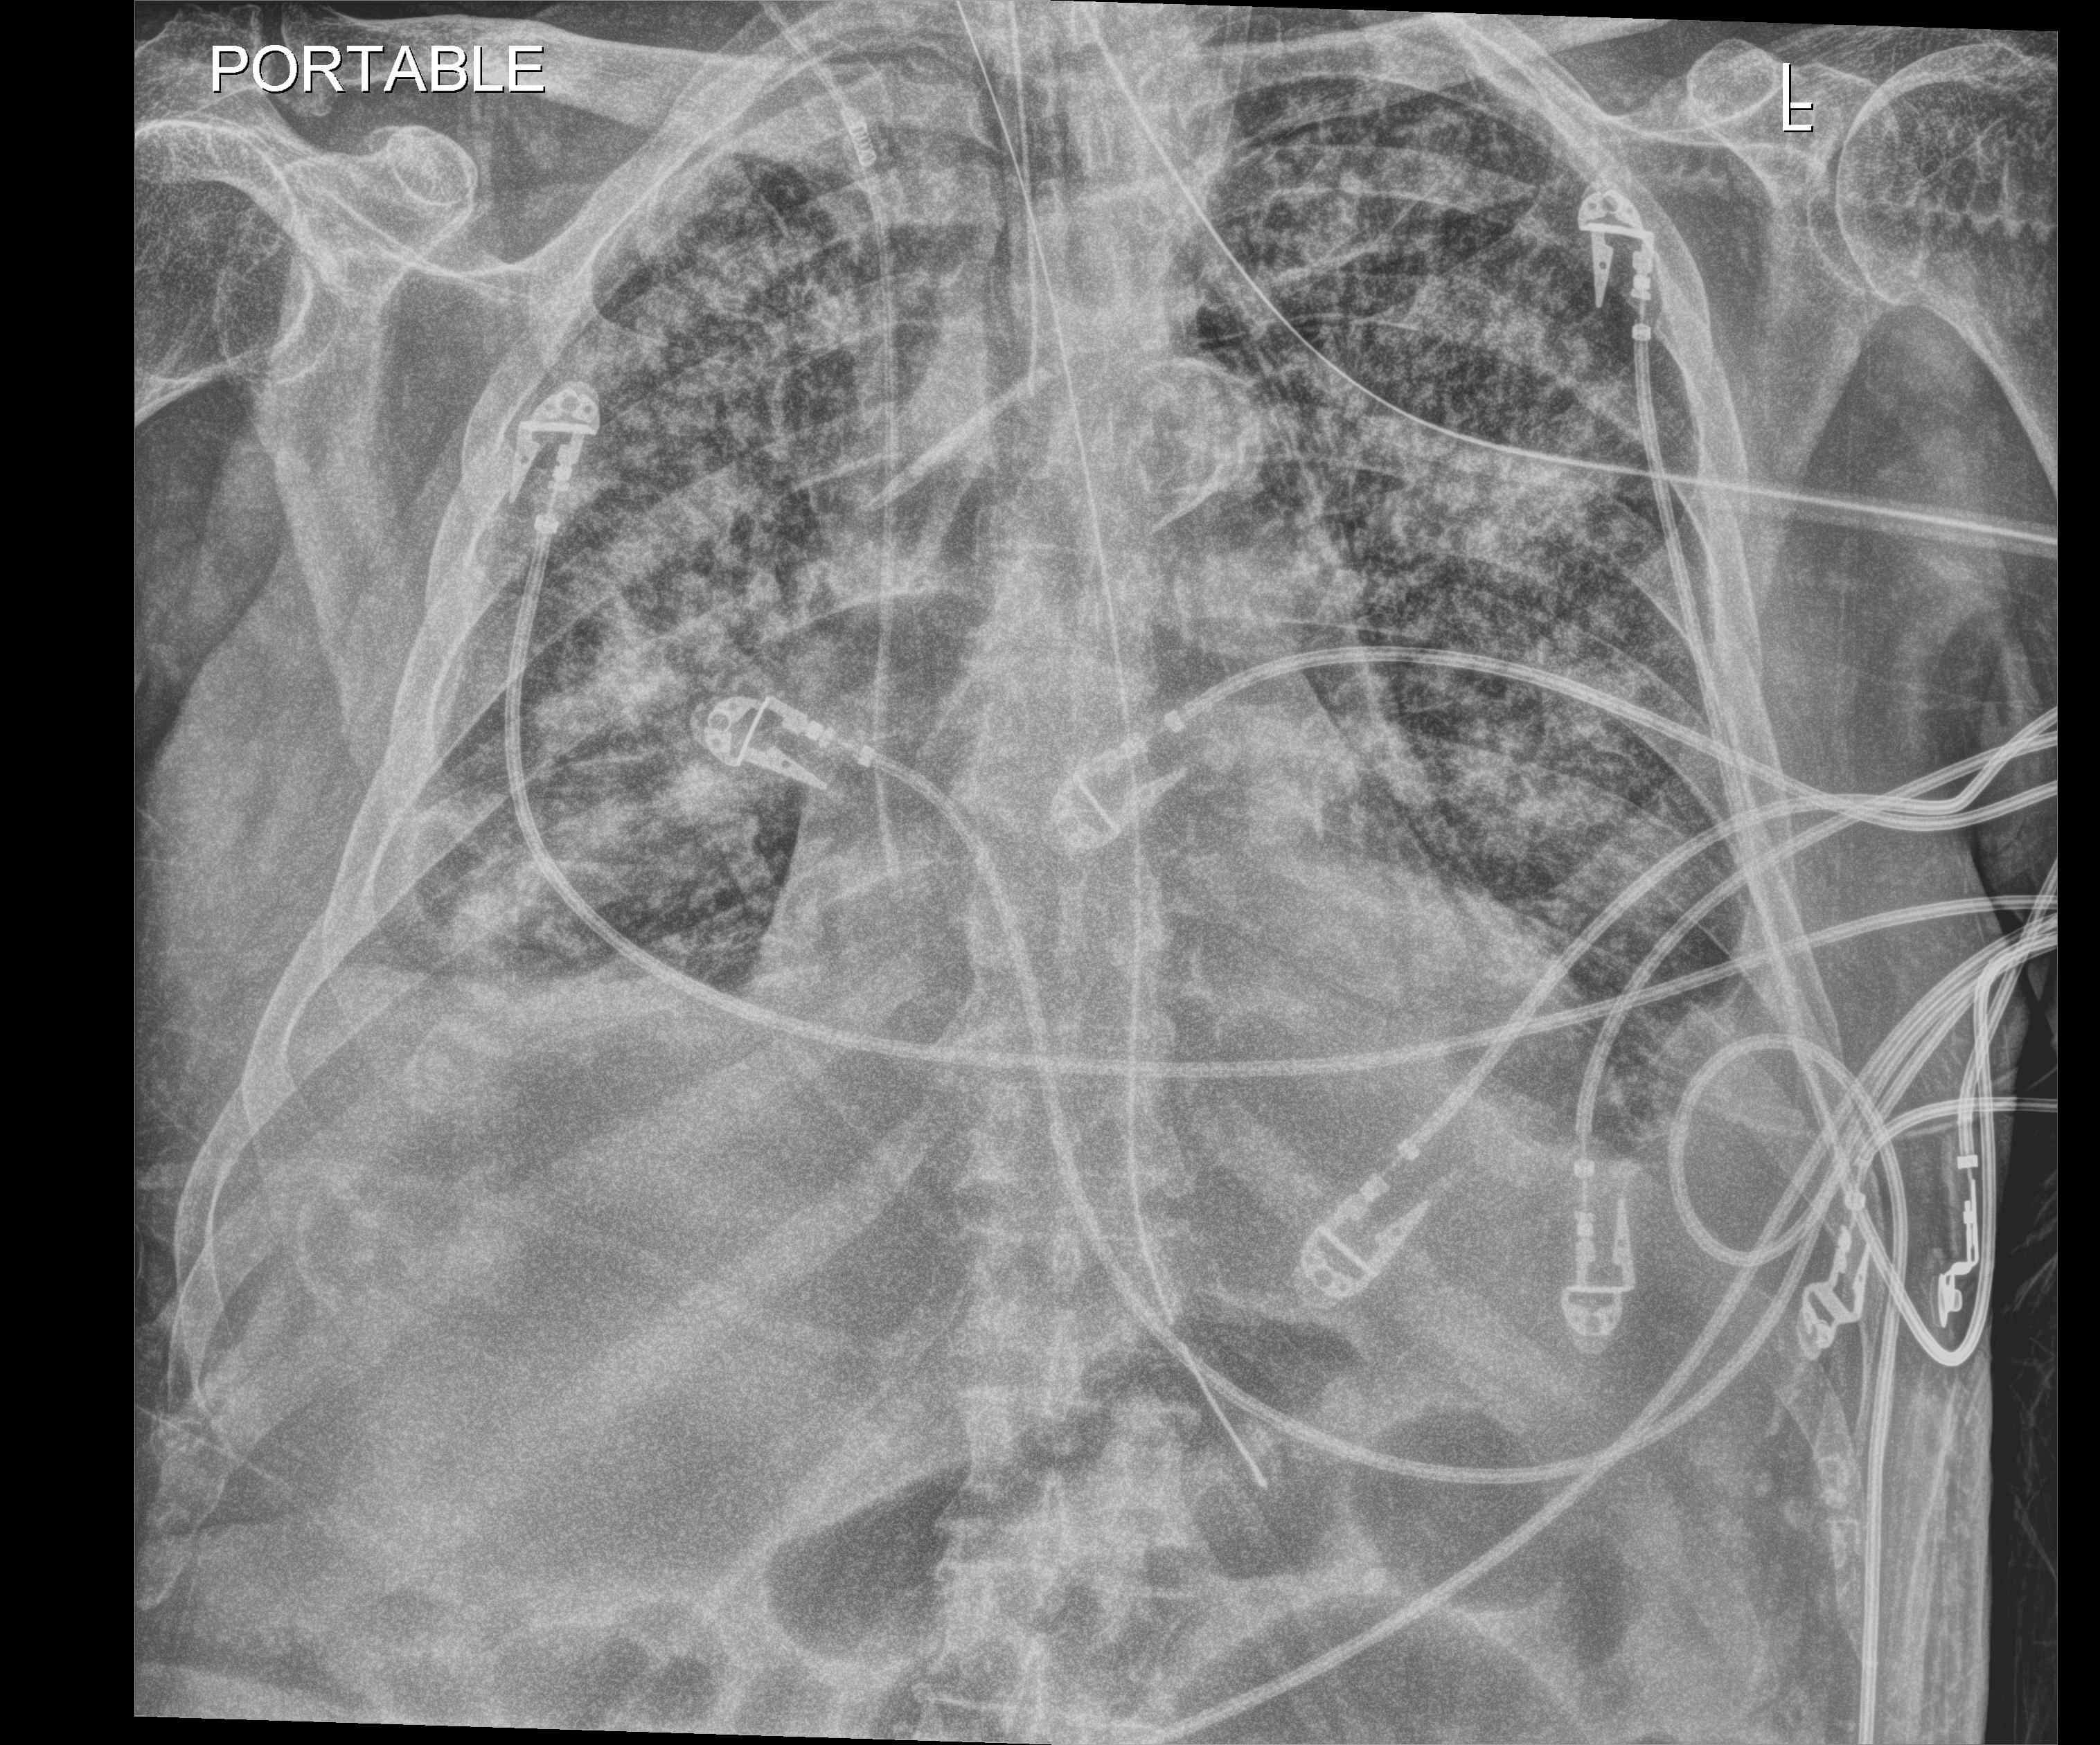
Portable chest radiograph; anteroposterior (AP) projection. Patient hospitalised with COVID-19; male, aged 75–90 years.
Admission-level facts for this patient (not findings on this image; timing relative to this image not recorded):
- mechanically ventilated during this hospital stay: yes